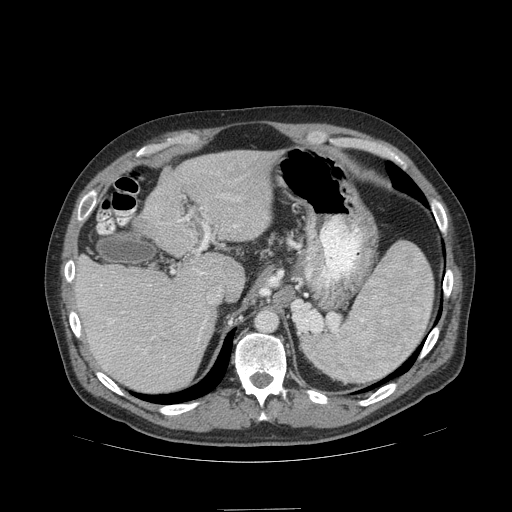
Contrast-enhanced abdominal CT (liver protocol), one axial slice. Position 74 of 99 along the scan axis. Reconstruction kernel STANDARD. Soft-tissue window (W 400 / L 40 HU). 512 × 512 image matrix, field of view 440 × 440 mm. From the clinical record (not read from this slice): diagnosis: hepatocellular carcinoma (patient treated with transarterial chemoembolisation; whether this scan precedes or follows treatment is not stated here); TNM stage (as recorded): Stage-I; Child-Pugh class: A.
Annotated regions visible in this slice (semi-automatic segmentation, software-assisted and operator-edited):
- liver parenchyma outside the tumour (the mass and vessels are separate outlines, so this box may not span the whole liver): bounding box (x1, y1, x2, y2) in pixels: (71, 150, 280, 392)
- liver vessels: (72, 198, 239, 358)